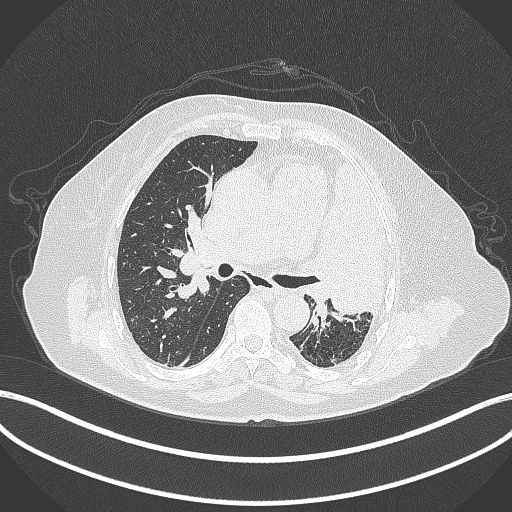
Chest CT, one axial slice. Position 231 of 399 along the scan axis. Reconstruction kernel B70f. 120 kVp. Lung window (W 1500 / L -600 HU). 1 mm slice thickness. 512 × 512 image matrix. Patient: female, 75 years. Case-level facts recorded for this patient, not image findings: clinical TNM (as recorded): T3 N3 M1.
Annotated regions visible in this slice (rectangle marked by the reading radiologist):
- lung tumour (recorded histology: adenocarcinoma): bounding box <310,157,389,320> (left, top, right, bottom; pixels)